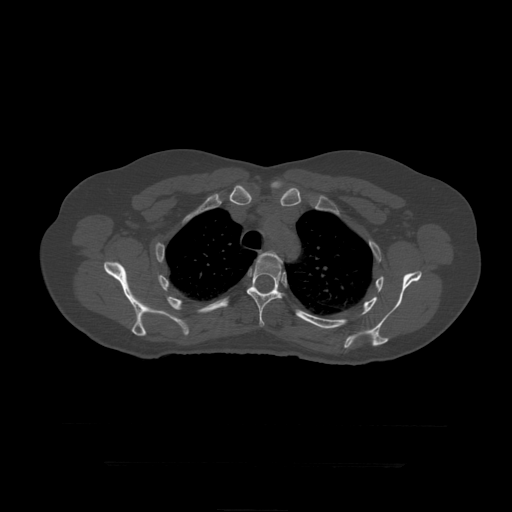
CT including the spine, one axial slice. Slice 336 of 399 in the series (ordered by position). 120 kVp. Bone window (W 1800 / L 400 HU). 1.25 mm slice thickness. 512 × 512 image matrix. Patient age 41 years. Case-level facts recorded for this patient, not image findings: primary cancer: breast.
Annotated regions visible in this slice (semi-automatic segmentation, software-assisted and operator-edited):
- T4 vertebra: bounding box (x1, y1, x2, y2) in pixels: (255, 251, 283, 270)
- T5 vertebra: (247, 255, 285, 327)